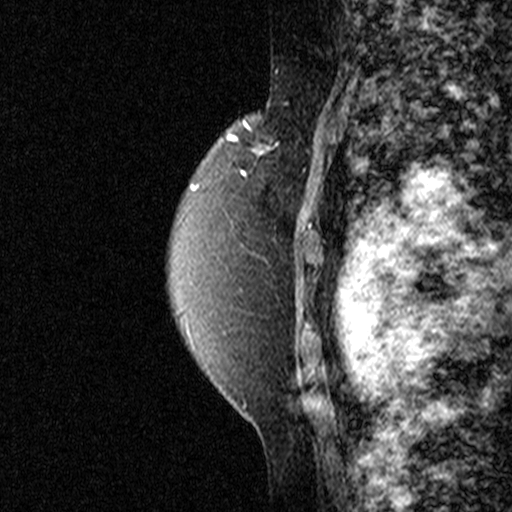
Breast MRI (dynamic contrast-enhanced), one sagittal slice. Position 33 of 44 along the scan axis. Dynamic contrast-enhanced study with each time point stored as its own series, time point 2 of 3 at this slice position (early post-contrast, ordered by acquisition time). 1.5 T. TE 4.5 ms, TR 11 ms. 512 × 512 image matrix, field of view 200 × 200 mm. Female patient, age 49 years. Case-level facts recorded for this patient, not image findings: setting: breast cancer imaged before/during neoadjuvant chemotherapy; receptor status: triple-negative.
Annotated regions visible in this slice (semi-automatic segmentation, software-assisted and operator-edited):
- analysis volume of interest (the breast-tissue region the enhancement analysis was run in; not a lesion): bounding box <256,100,335,197> (left, top, right, bottom; pixels)
- tumour enhancement mask (voxels above the 90 % enhancement threshold inside the analysis volume of interest): <264,145,267,148>